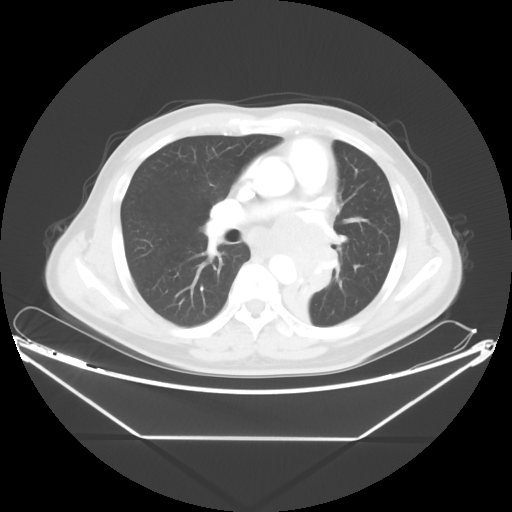
Chest CT, one axial slice; slice 25 of 48 in the series (ordered by position); reconstruction kernel STANDARD; lung window (W 1500 / L -600 HU); 5 mm slice thickness; 512 × 512 image matrix, field of view 438 × 438 mm. Patient: male, 58 years. From the clinical record (not read from this slice): clinical TNM (as recorded): T3 N3 M0.
Structures marked on this image (bounding box drawn by a radiologist):
- lung tumour (recorded histology: squamous cell carcinoma): bounding box (x1, y1, x2, y2) in pixels: (282, 249, 339, 329)